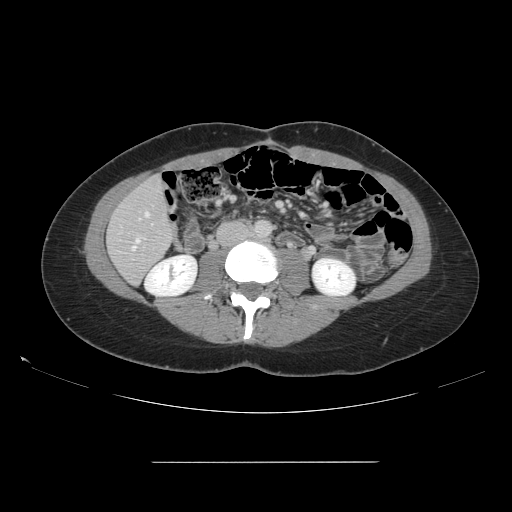
Contrast-enhanced abdominal CT, one axial slice. Position 41 of 151 along the scan axis. Intravenous contrast given. Soft-tissue window (W 400 / L 40 HU). 2.5 mm slice thickness. 512 × 512 image matrix. Female patient, age 46 years. From the clinical record (not read from this slice): diagnosis: colorectal cancer liver metastases, imaged before liver resection; multiple liver metastases: yes; largest metastasis: 3 cm; chemotherapy before resection: no.
Annotated regions visible in this slice (expert manual segmentation):
- hepatic veins: bounding box [x1, y1, x2, y2] px = [133, 212, 149, 250]
- liver: [108, 177, 174, 284]
- planned liver remnant (the part of the liver to remain after resection): [108, 177, 174, 284]